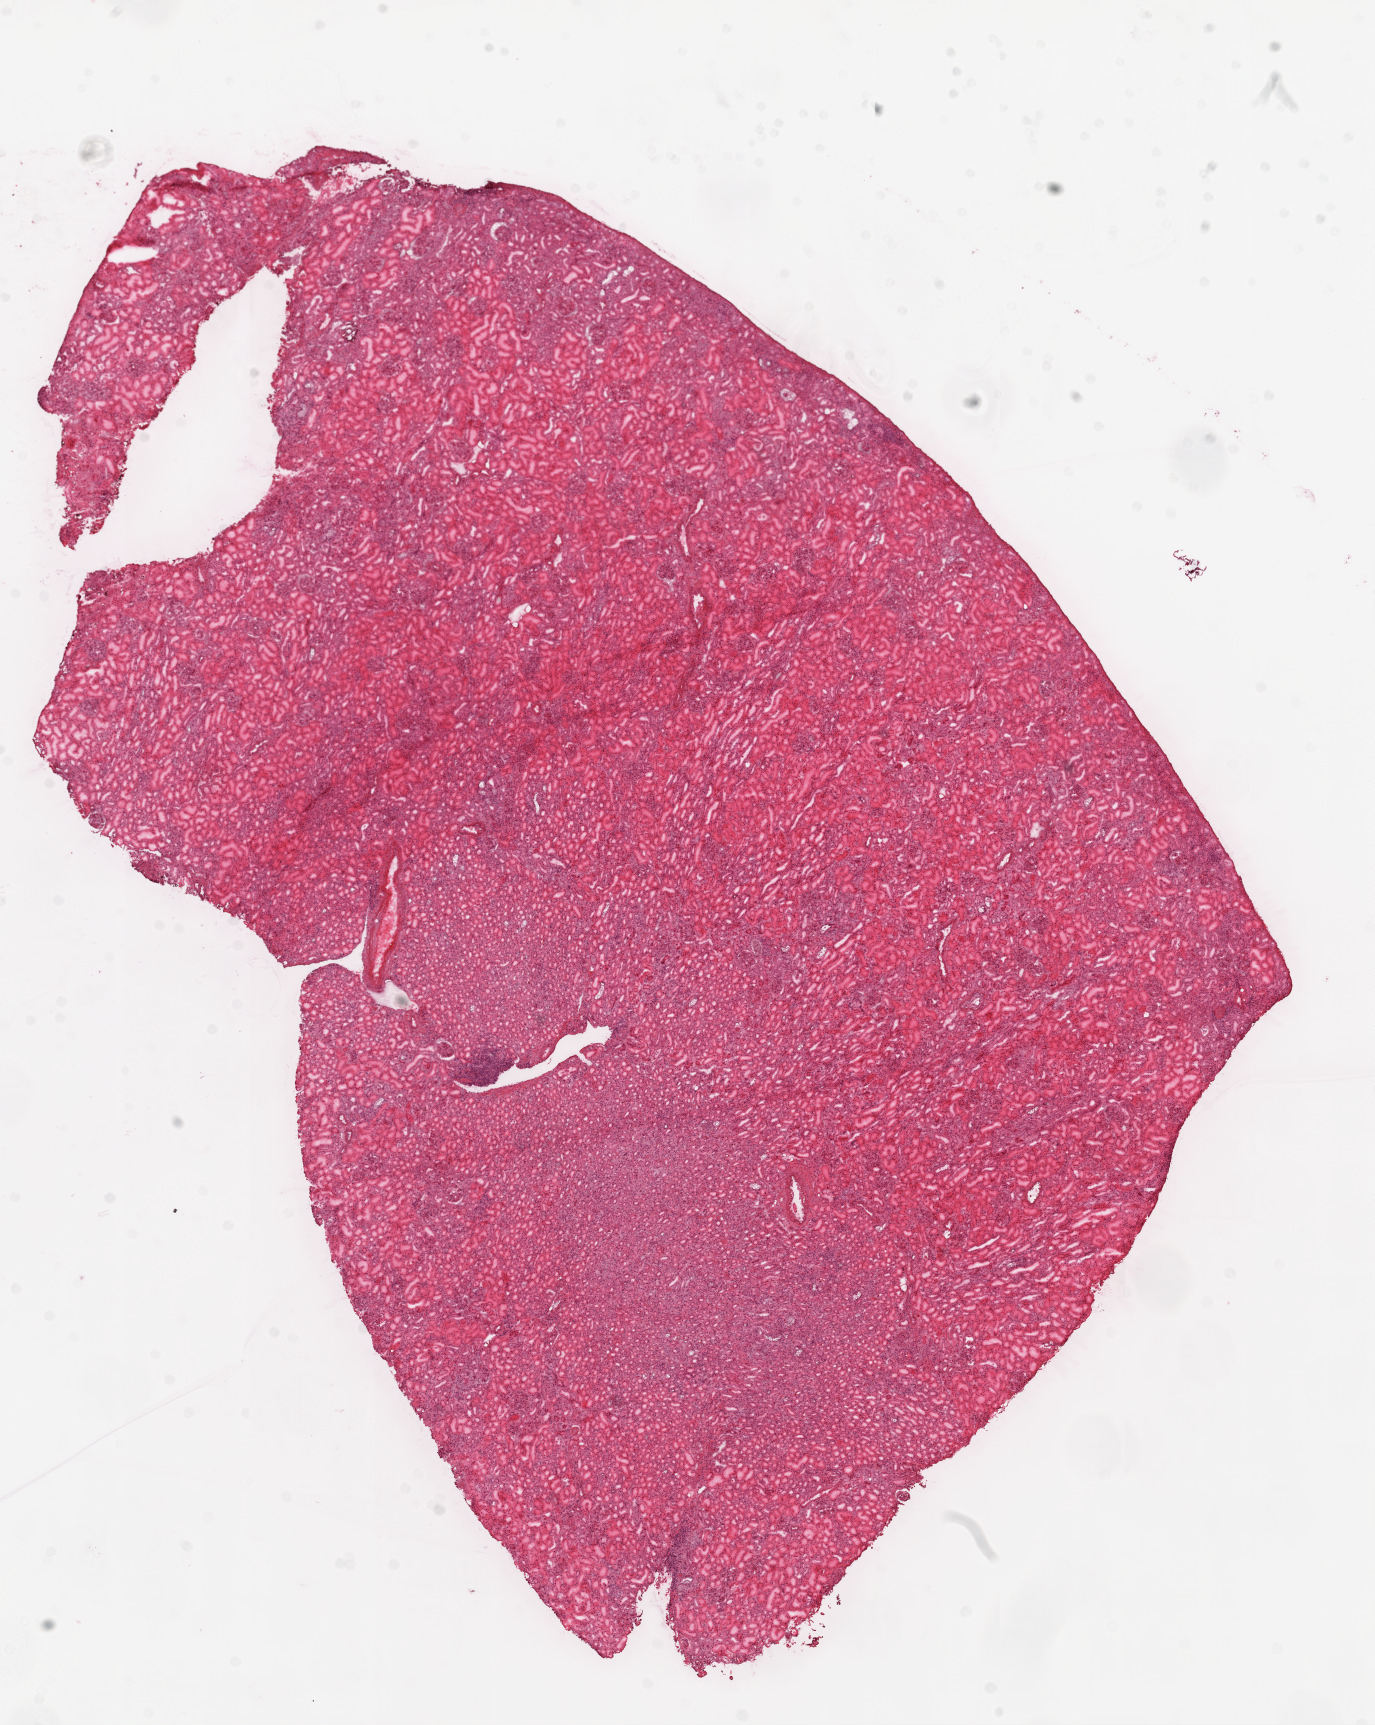
H&E-stained whole-slide image, a low-resolution overview of the entire scanned area, about 11.0 x 13.8 mm. Frozen section from the top of the tissue portion. Solid tissue normal (non-tumour tissue) sample from the kidney. Patient: male, age at initial diagnosis 58 years.
• this section: solid tissue normal (non-tumour) sample from the same patient
• patient diagnosis: Clear cell adenocarcinoma, NOS